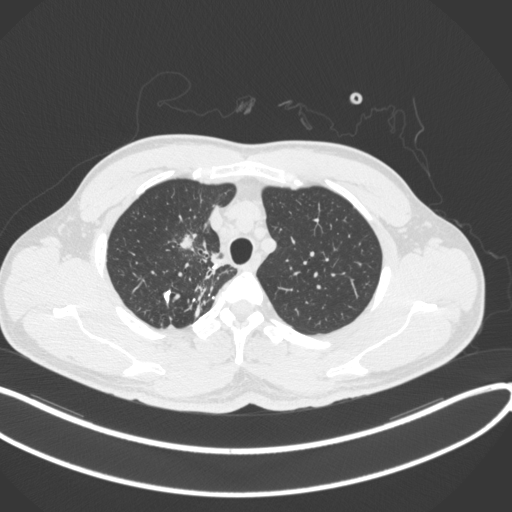
Chest CT, one axial slice; slice 303 of 391 in the series (ordered by position); 120 kVp; lung window (W 1500 / L -600 HU); 1 mm slice thickness; 512 × 512 image matrix, field of view 400 × 400 mm. Male patient, age 48 years. From the clinical record (not read from this slice): clinical TNM (as recorded): T1c N1 M1.
Structures marked on this image (rectangle marked by the reading radiologist):
- lung tumour (recorded histology: adenocarcinoma): bounding box [x1, y1, x2, y2] px = [171, 228, 202, 254]